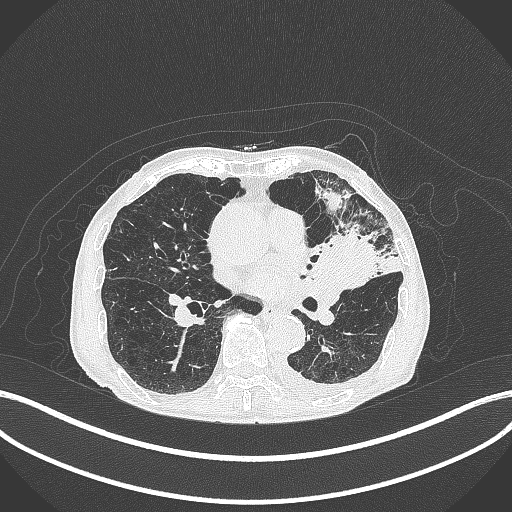
Chest CT, one axial slice; position 186 of 385 along the scan axis; lung window (W 1500 / L -600 HU); 1 mm slice thickness; 512 × 512 image matrix, field of view 400 × 400 mm. Male patient, age 90 years or older. Case-level facts recorded for this patient, not image findings: clinical TNM (as recorded): T2b N1 M0.
Structures marked on this image (rectangle marked by the reading radiologist):
- lung tumour (recorded histology: squamous cell carcinoma): bounding box (x1, y1, x2, y2) in pixels: (305, 225, 381, 293)